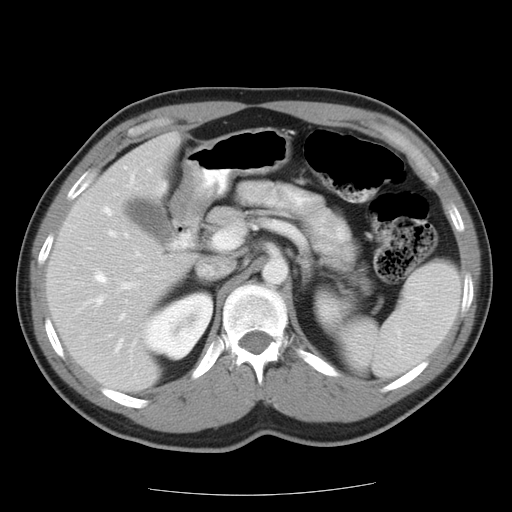
Contrast-enhanced abdominal CT, one axial slice; reconstruction kernel STANDARD; 120 kVp; intravenous contrast given; soft-tissue window (W 400 / L 40 HU); 7.5 mm slice thickness; 512 × 512 image matrix, field of view 359 × 359 mm. Male patient, age 41 years. Case-level facts recorded for this patient, not image findings: diagnosis: colorectal cancer liver metastases, imaged before liver resection; multiple liver metastases: no; largest metastasis: 2.7 cm; disease in both lobes: no.
Annotated regions visible in this slice (manually delineated by an expert):
- hepatic veins: bounding box [x1, y1, x2, y2] px = [90, 208, 123, 351]
- liver: [48, 137, 181, 392]
- planned liver remnant (the part of the liver to remain after resection): [48, 138, 181, 363]
- portal vein (with intrahepatic branches): [110, 232, 116, 237]